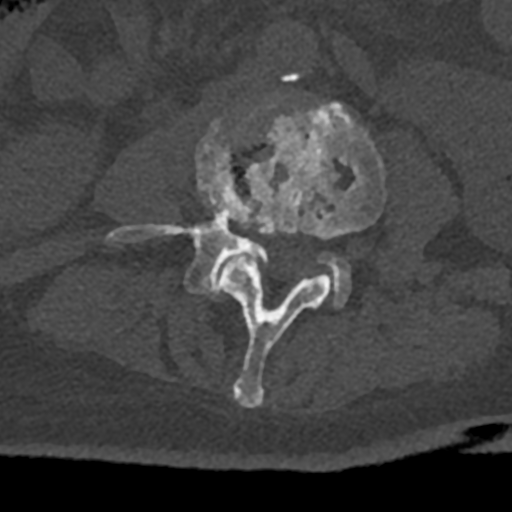
CT including the spine, one axial slice. Slice 293 of 797 in the series (ordered by position). 120 kVp. Bone window (W 1800 / L 400 HU). 512 × 512 image matrix, field of view 160 × 160 mm. Patient: male, 74 years. From the clinical record (not read from this slice): primary cancer: renal; vertebrae with lytic lesions (as recorded): T10, L1, L2, L3, L4, L5.
Annotated regions visible in this slice (semi-automatic segmentation, software-assisted and operator-edited):
- L3 vertebra: box from (x=220, y=103) to (x=386, y=408) px
- L4 vertebra: (x=107, y=120)–(x=350, y=308)